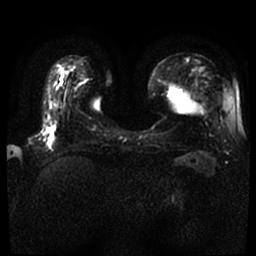
Breast MRI, one axial slice; slice 12 of 59 in the series (ordered by position); diffusion-weighted series; image 2 of 4 stored at this slice position (different b-values; order by instance number); 1.5 T; 4 mm slice thickness; 256 × 256 image matrix. Female patient.
Annotated regions visible in this slice (expert manual segmentation):
- tumour on diffusion-weighted imaging: bounding box (x1, y1, x2, y2) in pixels: (46, 127, 54, 140)